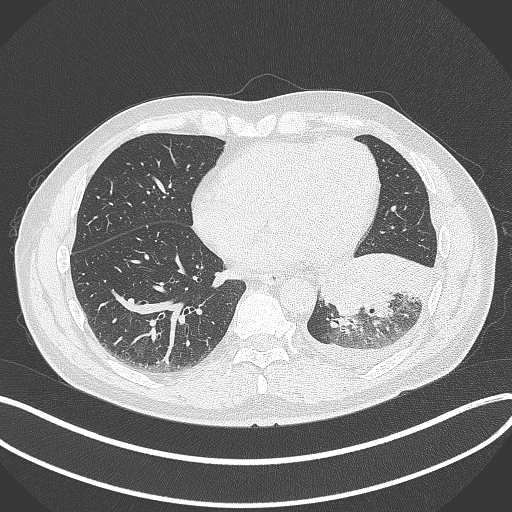
Chest CT, one axial slice. Position 123 of 342 along the scan axis. 120 kVp. Lung window (W 1500 / L -600 HU). 1 mm slice thickness. 512 × 512 image matrix. Male patient, age 58 years. From the clinical record (not read from this slice): clinical TNM (as recorded): T3 N1 M1b.
Annotated regions visible in this slice (rectangle marked by the reading radiologist):
- lung tumour (recorded histology: small cell carcinoma): bounding box [x1, y1, x2, y2] px = [312, 249, 435, 324]